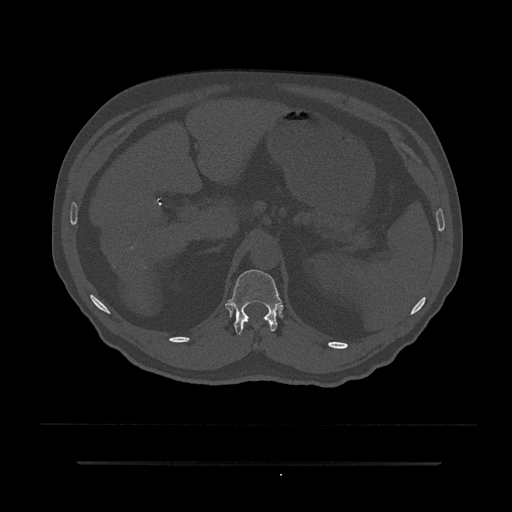
CT including the spine, one axial slice. Slice 222 of 797 in the series (ordered by position). 120 kVp. Bone window (W 1800 / L 400 HU). 512 × 512 image matrix, field of view 464 × 464 mm. Patient: male, 59 years. From the clinical record (not read from this slice): primary cancer: bile ducts.
Structures marked on this image (semi-automatically segmented with operator editing):
- T12 vertebra: bounding box <228,269,282,335> (left, top, right, bottom; pixels)